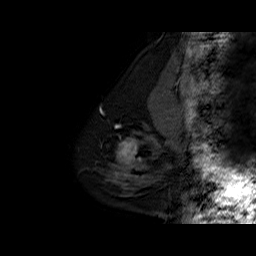
Breast MRI (dynamic contrast-enhanced), one sagittal slice; position 12 of 60 along the scan axis; dynamic contrast-enhanced series, time point 2 of 6 at this slice position (early post-contrast); 1.5 T; TE 6.3 ms, TR 32.5 ms; 256 × 256 image matrix, field of view 200 × 200 mm. Female patient. From the clinical record (not read from this slice): setting: breast cancer imaged before/during neoadjuvant chemotherapy; receptor status: triple-negative.
Outlined on this slice (semi-automatically segmented with operator editing):
- analysis volume of interest (the breast-tissue region the enhancement analysis was run in; not a lesion): box from (x=102, y=127) to (x=162, y=186) px
- tumour enhancement mask (voxels above the 100 % enhancement threshold inside the analysis volume of interest): (x=118, y=139)–(x=156, y=164)